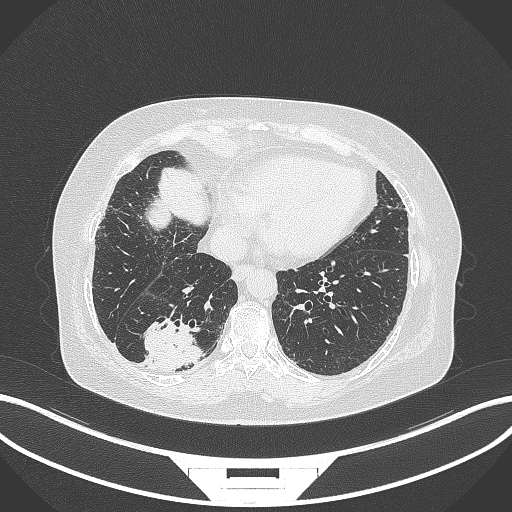
Chest CT, one axial slice. Position 66 of 296 along the scan axis. Reconstruction kernel B70f. 120 kVp. Lung window (W 1500 / L -600 HU). 1 mm slice thickness. 512 × 512 image matrix, field of view 400 × 400 mm. Patient: female, 65 years. From the clinical record (not read from this slice): clinical TNM (as recorded): T2b N1 M0; histopathological grade: G1.
Structures marked on this image (rectangle marked by the reading radiologist):
- lung tumour (recorded histology: adenocarcinoma): box from (x=135, y=317) to (x=208, y=371) px